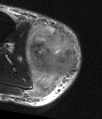
MRI of an extremity soft-tissue mass, one axial slice. T2-weighted fat-saturated. MR volume resampled by the dataset authors to the PET/CT grid (not the native acquisition matrix). 3.27 mm slice thickness. 102 × 119 image matrix, field of view 100 × 116 mm. Male patient. Case-level facts recorded for this patient, not image findings: histological type: pleiomorphic liposarcoma; grade: high; site of the primary tumour: right calf.
Structures marked on this image (expert contour drawn on MRI and transferred to this co-registered scan by the dataset authors):
- gross tumour volume including surrounding oedema: bounding box [x1, y1, x2, y2] px = [26, 24, 77, 100]
- gross tumour volume (mass): [30, 30, 77, 79]